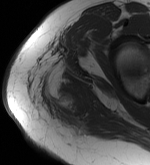
MRI of an extremity soft-tissue mass, one axial slice. Position 44 of 56 along the scan axis. MR volume resampled by the dataset authors to the PET/CT grid (not the native acquisition matrix). 3.27 mm slice thickness. 150 × 165 image matrix, field of view 146 × 161 mm. Female patient. From the clinical record (not read from this slice): histological type: epithelioid sarcoma with vascular differentiation; site of the primary tumour: right buttock.
Annotated regions visible in this slice (expert contour drawn on MRI and transferred to this co-registered scan by the dataset authors):
- gross tumour volume (mass): bounding box (x1, y1, x2, y2) in pixels: (43, 90, 81, 98)